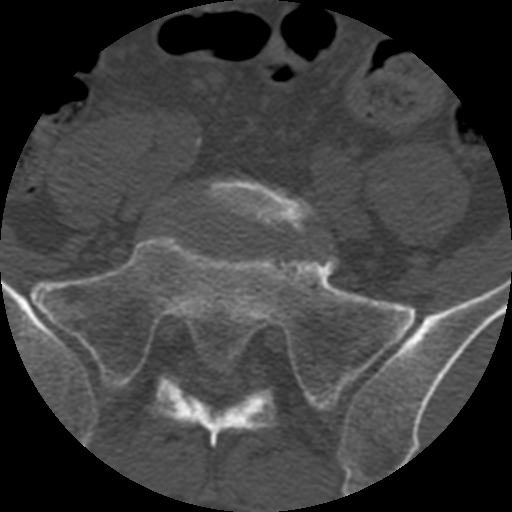
CT including the spine, one axial slice; position 235 of 399 along the scan axis; reconstruction kernel STANDARD; bone window (W 1800 / L 400 HU); 1.25 mm slice thickness; 512 × 512 image matrix. Patient age 71 years. From the clinical record (not read from this slice): primary cancer: prostate.
Annotated regions visible in this slice (semi-automatically segmented with operator editing):
- L5 vertebra: bounding box [x1, y1, x2, y2] px = [203, 180, 318, 236]